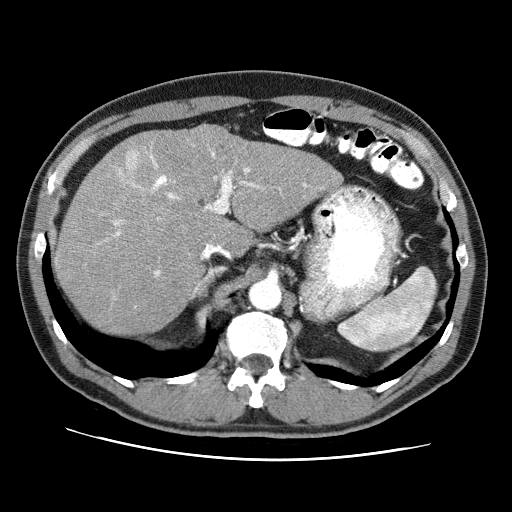
Contrast-enhanced abdominal CT (liver protocol), one axial slice. Position 50 of 71 along the scan axis. Reconstruction kernel STANDARD. 120 kVp. Soft-tissue window (W 400 / L 40 HU). 2.5 mm slice thickness. 512 × 512 image matrix. Case-level facts recorded for this patient, not image findings: diagnosis: hepatocellular carcinoma (patient treated with transarterial chemoembolisation; whether this scan precedes or follows treatment is not stated here); TNM stage (as recorded): Stage-II.
Structures marked on this image (semi-automatic segmentation, software-assisted and operator-edited):
- abdominal aorta: bounding box (x1, y1, x2, y2) in pixels: (251, 281, 279, 309)
- liver parenchyma outside the tumour (the mass and vessels are separate outlines, so this box may not span the whole liver): (54, 124, 340, 334)
- mass: (119, 149, 144, 186)
- liver vessels: (115, 153, 306, 276)